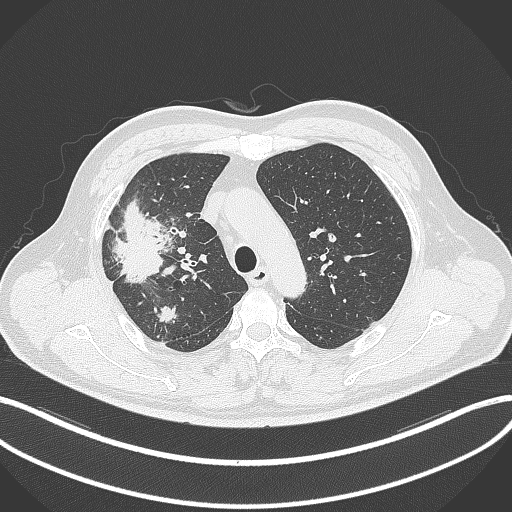
Chest CT, one axial slice. Position 248 of 348 along the scan axis. Reconstruction kernel B70f. Lung window (W 1500 / L -600 HU). 512 × 512 image matrix, field of view 400 × 400 mm. Patient: male, 55 years. From the clinical record (not read from this slice): clinical TNM (as recorded): T3 N2 M1.
Annotated regions visible in this slice (rectangle marked by the reading radiologist):
- lung tumour (recorded histology: adenocarcinoma): bounding box <110,194,172,287> (left, top, right, bottom; pixels)